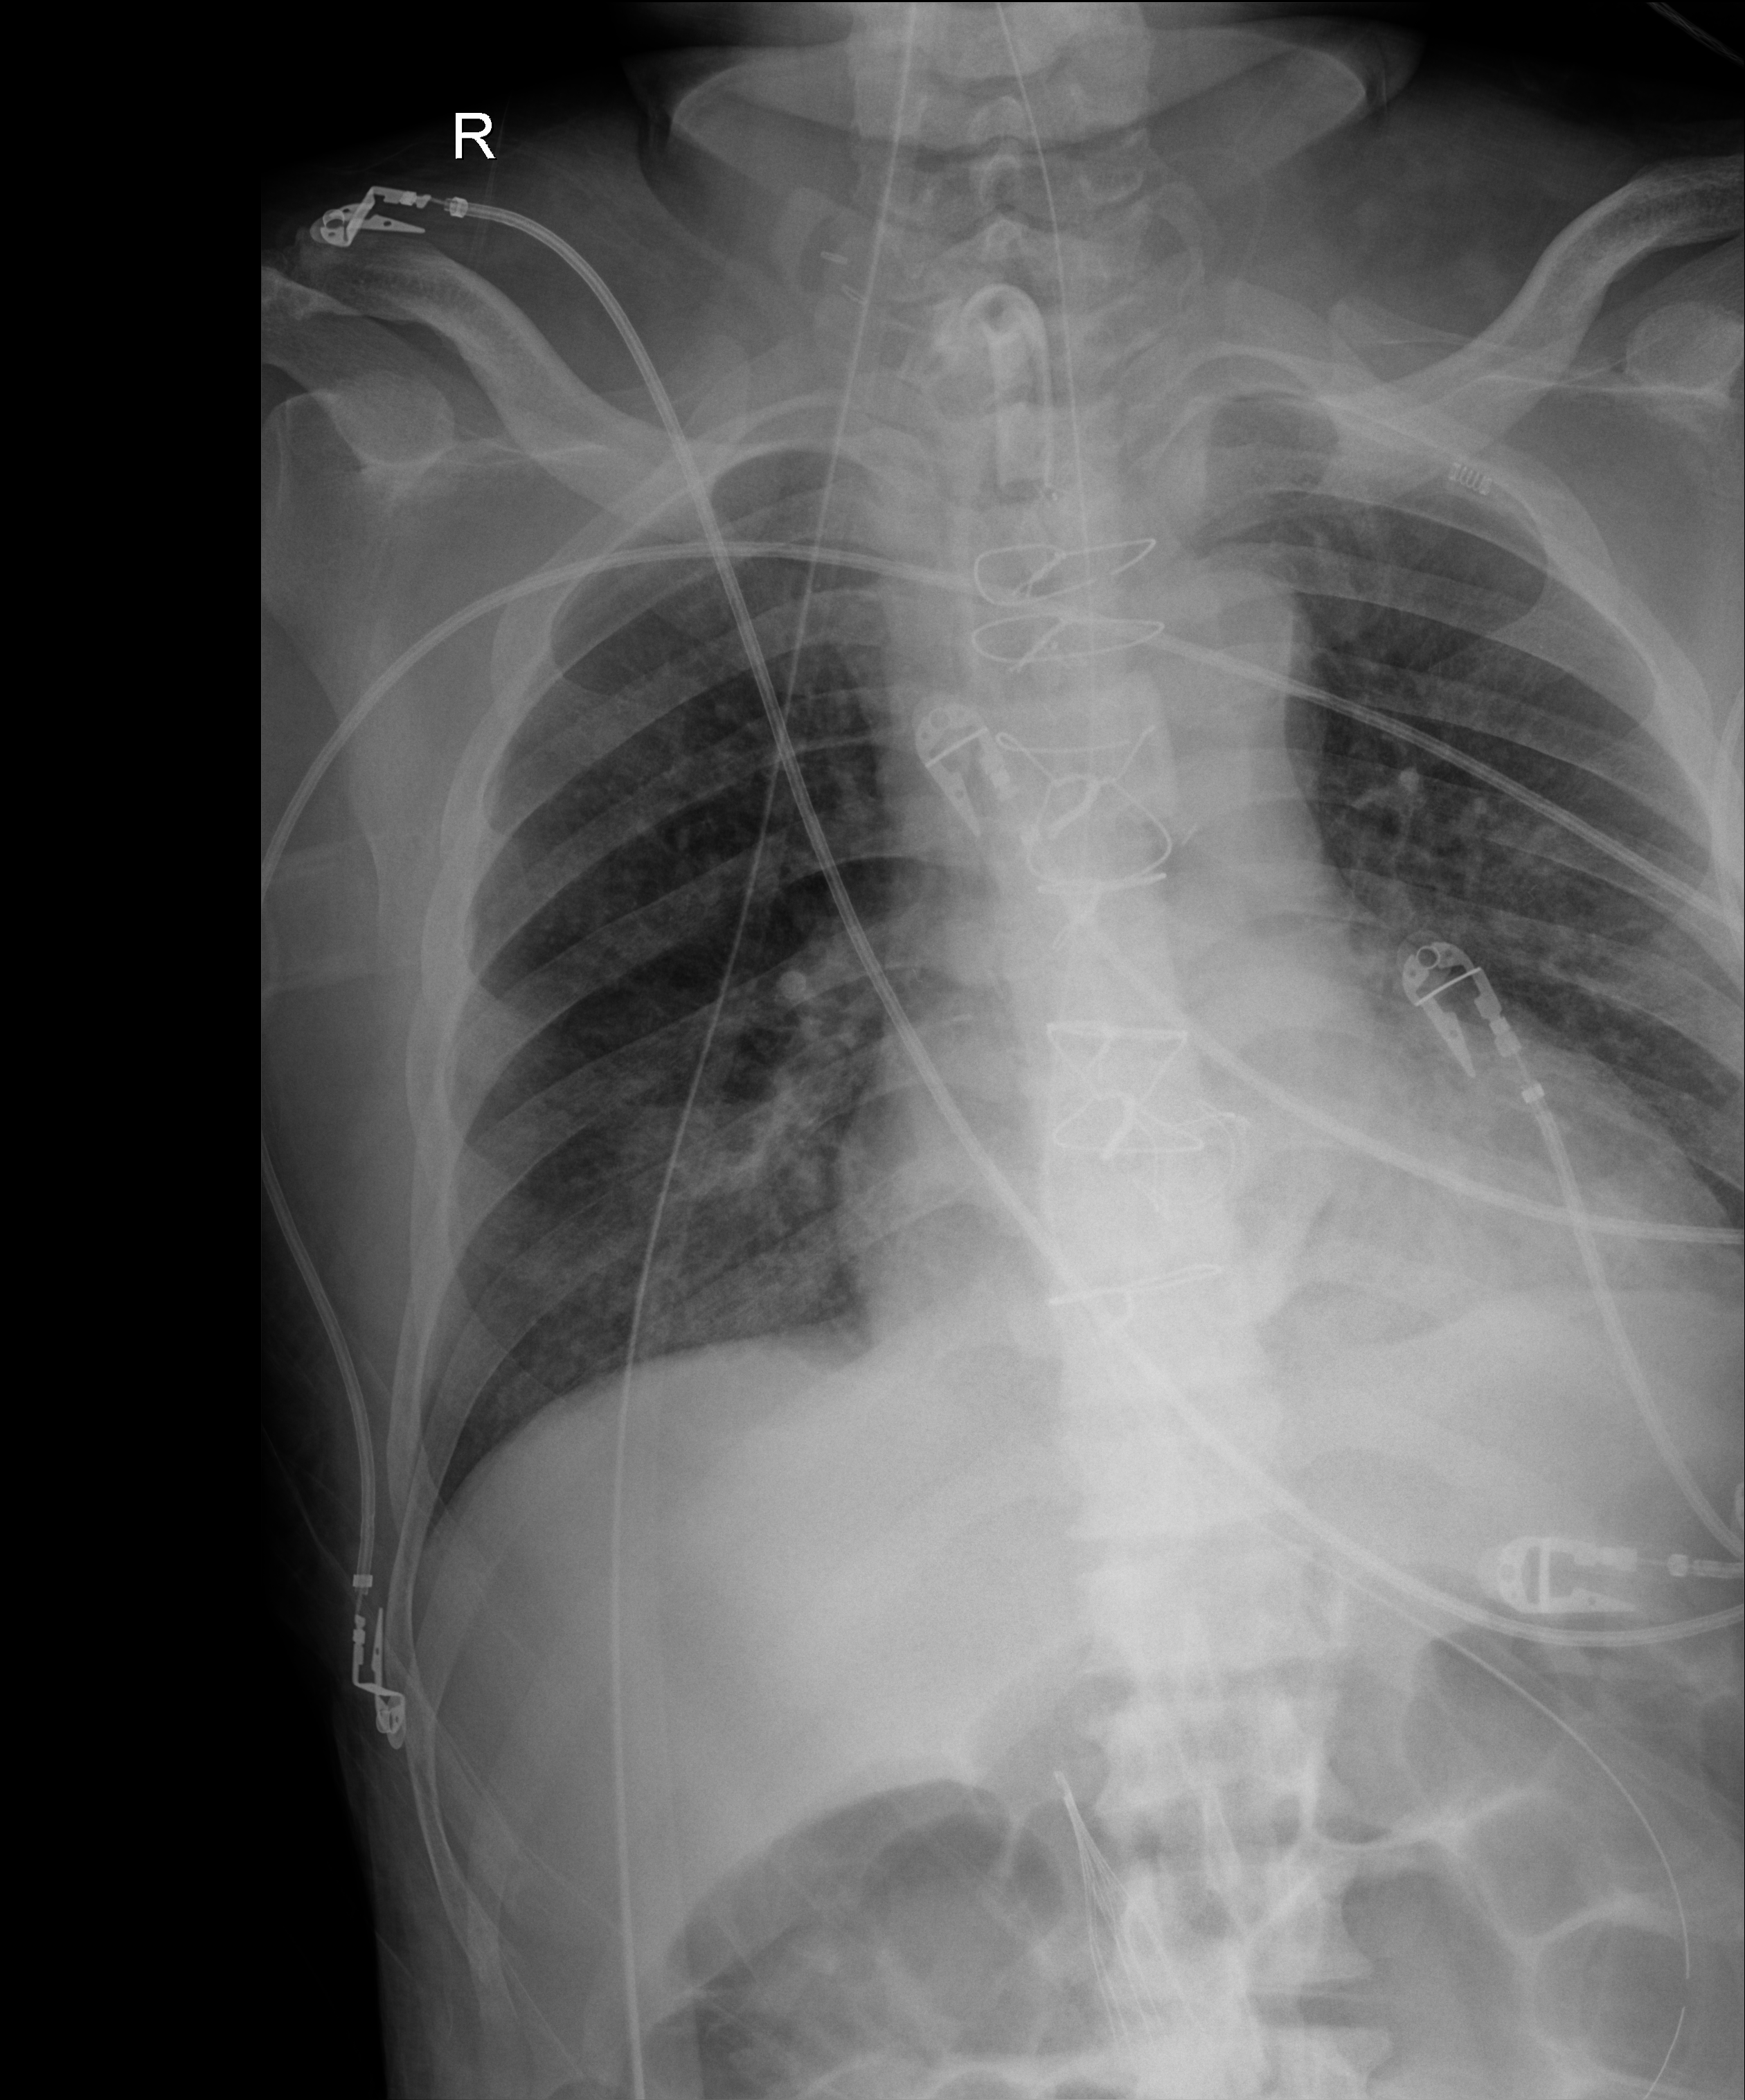
Chest X-ray (portable), anteroposterior (AP) projection. Patient hospitalised with COVID-19; male, aged 60–74 years.
Admission-level facts for this patient (not findings on this image; timing relative to this image not recorded):
- COPD (admission record): no
- mechanically ventilated during this hospital stay: yes